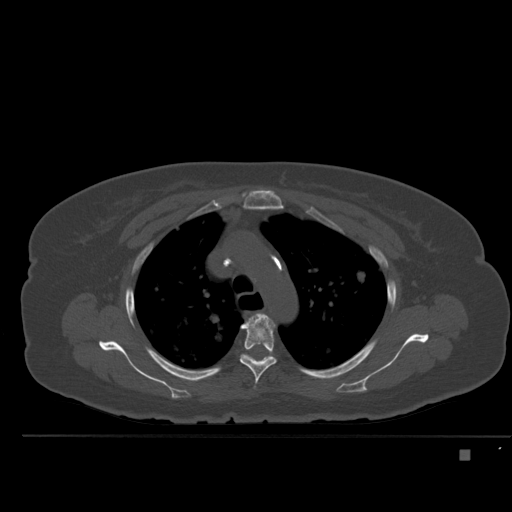
CT including the spine, one axial slice; slice 366 of 477 in the series (ordered by position); bone window (W 1800 / L 400 HU); 512 × 512 image matrix. Patient: female, 74 years. Case-level facts recorded for this patient, not image findings: primary cancer: colon.
Structures marked on this image (semi-automatically segmented with operator editing):
- T3 vertebra: box from (x=266, y=316) to (x=275, y=326) px
- T4 vertebra: (x=240, y=313)–(x=276, y=388)
- T5 vertebra: (x=243, y=354)–(x=254, y=359)